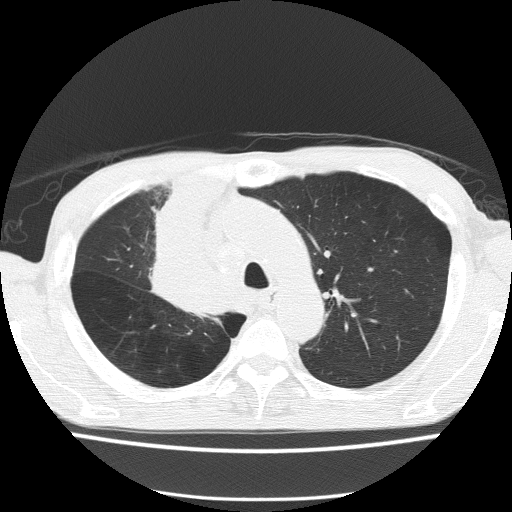
Low-dose screening chest CT, one axial slice; slice 109 of 150 in the series (ordered by position); reconstruction kernel FC51; 120 kVp; lung window (W 1500 / L -600 HU); 2 mm slice thickness; 512 × 512 image matrix.
Structures marked on this image (manually delineated by an expert):
- lesion 1 (tumor, hilum of right lung): bounding box [x1, y1, x2, y2] px = [155, 176, 234, 313]